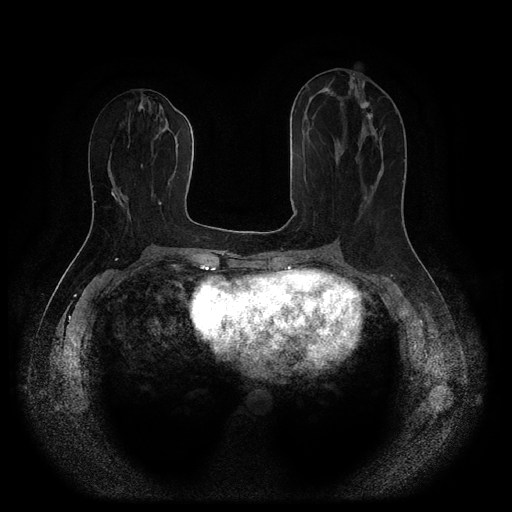
Breast MRI (dynamic contrast-enhanced, multi-phase), one axial slice. Position 43 of 116 along the scan axis. Dynamic contrast-enhanced series, time point 2 of 5 at this slice position (early post-contrast). 1.5 T. TE 2.6 ms, TR 5.3 ms. 2.2 mm slice thickness. 512 × 512 image matrix, field of view 360 × 360 mm. Patient: female, 53 years.
Structures marked on this image (semi-automatically segmented with operator editing):
- breast lesion (labelled 'tumour' in the annotation; benign lesions carry a separate 'benign' label): box from (x=361, y=102) to (x=373, y=119) px